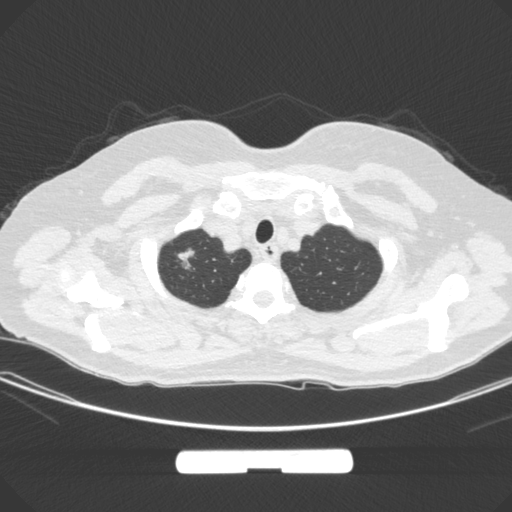
Chest CT, one axial slice; position 263 of 295 along the scan axis; lung window (W 1500 / L -600 HU); 512 × 512 image matrix, field of view 369 × 369 mm. Female patient, age 58 years. From the clinical record (not read from this slice): clinical TNM (as recorded): T1b N0 M0; histopathological grade: G2-3.
Outlined on this slice (rectangle marked by the reading radiologist):
- lung tumour (recorded histology: adenocarcinoma): bounding box [x1, y1, x2, y2] px = [175, 242, 201, 278]